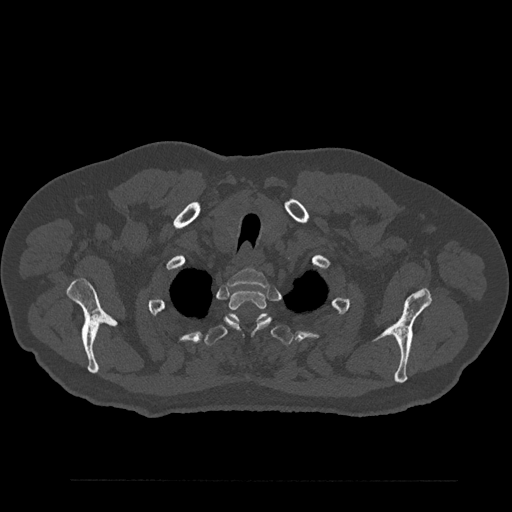
CT including the spine, one axial slice. Position 711 of 797 along the scan axis. Bone window (W 1800 / L 400 HU). 0.5 mm slice thickness. 512 × 512 image matrix, field of view 430 × 430 mm. Male patient, age 61 years. Case-level facts recorded for this patient, not image findings: primary cancer: prostate.
Outlined on this slice (semi-automatically segmented with operator editing):
- T1 vertebra: bounding box (x1, y1, x2, y2) in pixels: (227, 269, 268, 287)
- T2 vertebra: (224, 290, 272, 329)
- T3 vertebra: (205, 313, 293, 345)